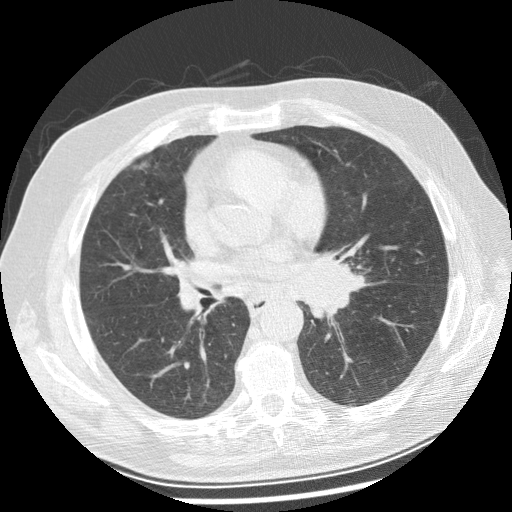
Low-dose screening chest CT, axial slice; baseline screening round; lung window (W 1500 / L -600 HU); 2.5 mm slice thickness; 120 kVp; 512 × 512 image matrix, field of view 360 × 360 mm. Male participant, aged 70 years at enrolment. Current smoker at enrolment.
Expert-annotated lung lesion, bounding box (x1, y1, x2, y2) in pixels: (290, 241, 373, 321). No non-calcified nodule or mass ≥4 mm was recorded by the screening reader at this exam. Later outcome: lung cancer diagnosed 29 days after this screen — squamous cell carcinoma, keratinizing, NOS, left main stem bronchus, moderately differentiated (G2), stage IIIB (AJCC 6th edition), 40 mm at pathology.